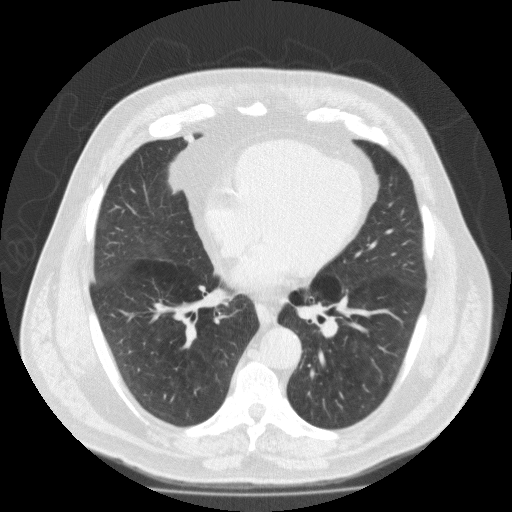
Low-dose screening chest CT, one axial slice. Slice 87 of 188 in the series (ordered by position). Reconstruction kernel FC10. Lung window (W 1500 / L -600 HU). 2 mm slice thickness. 512 × 512 image matrix, field of view 420 × 420 mm.
Outlined on this slice (manually delineated by an expert):
- lesion 1 (tumor, lower lobe of right lung): bounding box (x1, y1, x2, y2) in pixels: (169, 136, 198, 190)